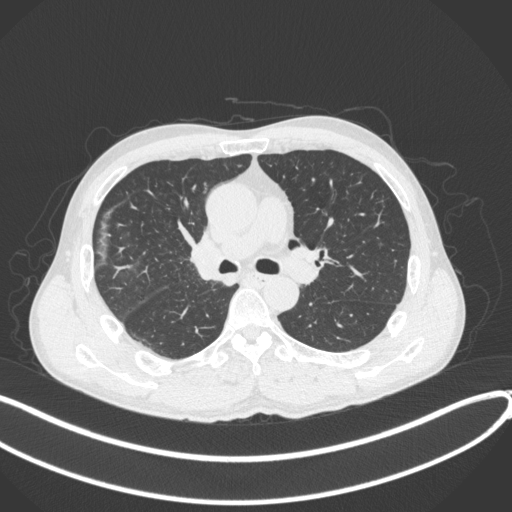
Chest CT, one axial slice. Position 235 of 409 along the scan axis. Reconstruction kernel B31f. 120 kVp. Lung window (W 1500 / L -600 HU). 1 mm slice thickness. 512 × 512 image matrix, field of view 400 × 400 mm. Patient: male, 53 years. From the clinical record (not read from this slice): clinical TNM (as recorded): T1b N0 M0.
Outlined on this slice (rectangle marked by the reading radiologist):
- lung tumour (recorded histology: squamous cell carcinoma): bounding box (x1, y1, x2, y2) in pixels: (184, 228, 226, 286)